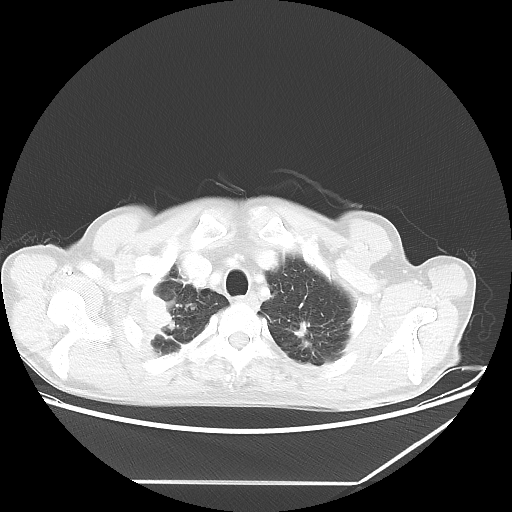
Chest CT, one axial slice; slice 57 of 65 in the series (ordered by position); reconstruction kernel LUNG; lung window (W 1500 / L -600 HU); 5 mm slice thickness; 512 × 512 image matrix, field of view 397 × 397 mm. Patient: male, 68 years. From the clinical record (not read from this slice): clinical TNM (as recorded): T3 N3 M0.
Outlined on this slice (bounding box drawn by a radiologist):
- lung tumour (recorded histology: adenocarcinoma): bounding box [x1, y1, x2, y2] px = [123, 287, 172, 343]